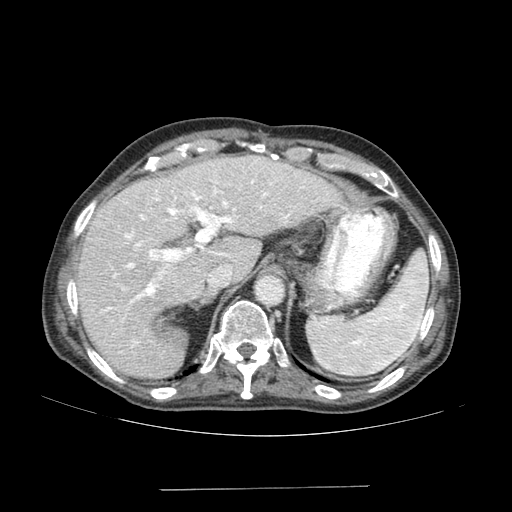
Contrast-enhanced abdominal CT (liver protocol), one axial slice; position 114 of 192 along the scan axis; reconstruction kernel SOFT; 120 kVp; soft-tissue window (W 400 / L 40 HU); 512 × 512 image matrix, field of view 400 × 400 mm. Case-level facts recorded for this patient, not image findings: diagnosis: hepatocellular carcinoma (patient treated with transarterial chemoembolisation; whether this scan precedes or follows treatment is not stated here); TNM stage (as recorded): Stage-IVA; Child-Pugh class: A.
Structures marked on this image (semi-automatically segmented with operator editing):
- liver parenchyma outside the tumour (the mass and vessels are separate outlines, so this box may not span the whole liver): bounding box <76,156,344,378> (left, top, right, bottom; pixels)
- liver vessels: <105,160,303,343>